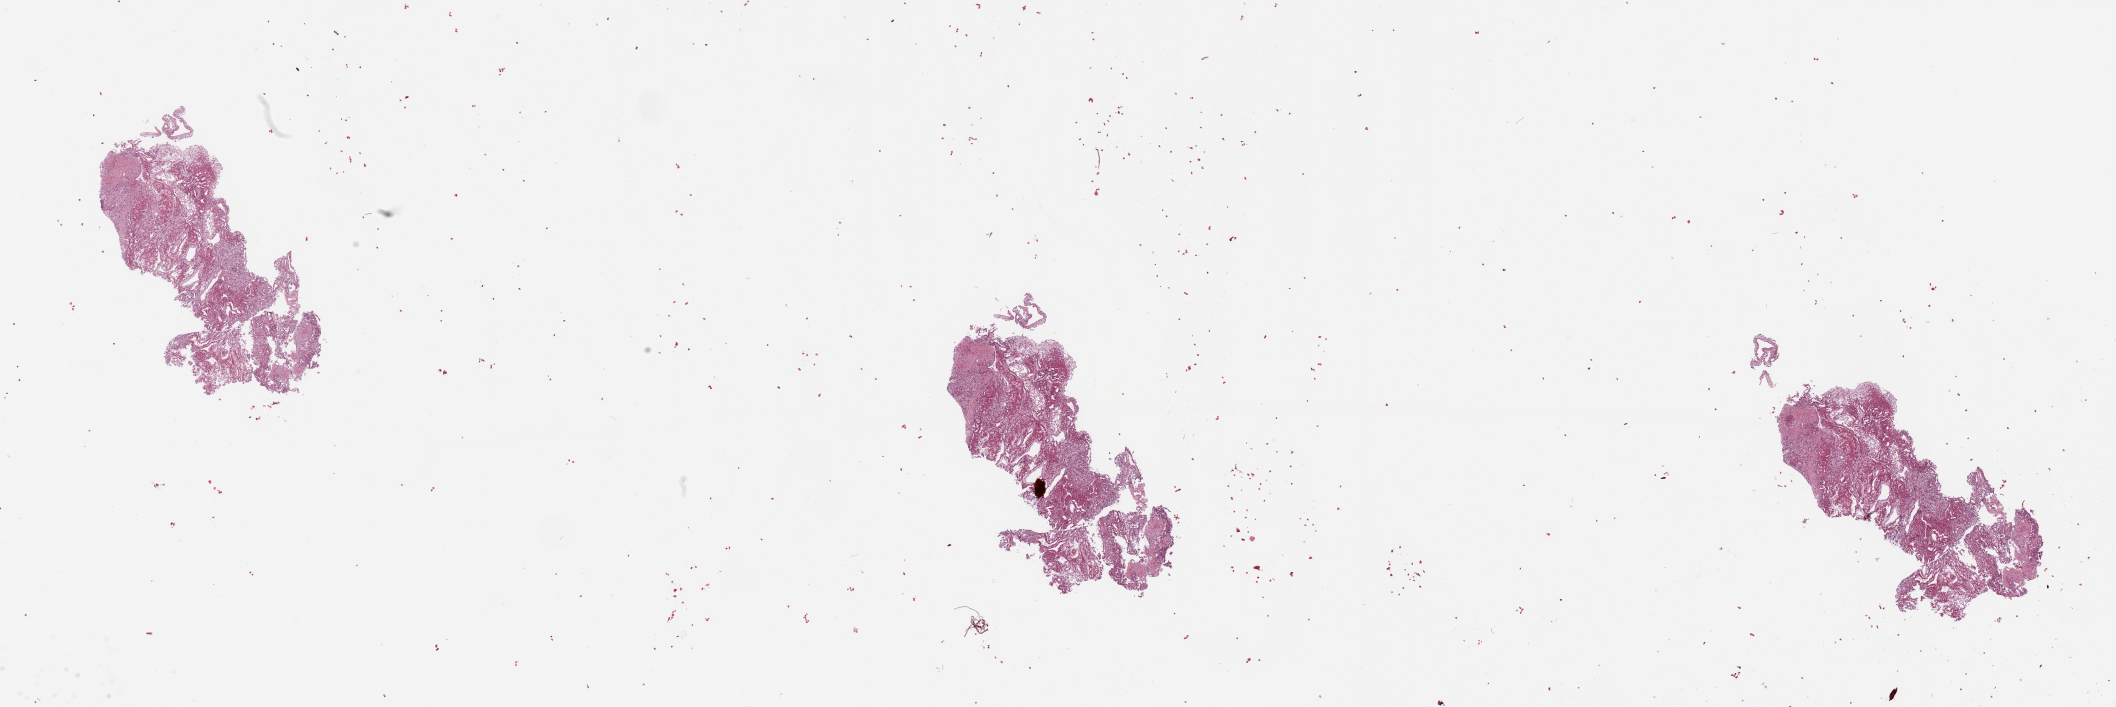
Digitized H&E-stained tissue section (whole slide), whole scanned area (about 33.5 x 11.2 mm, acquisition: 20x scan) shown as a low-resolution overview. Kidney, tumour tissue. 69-year-old male patient. Histologic grade: G3 (poorly differentiated).
• AJCC pathologic stage: III
• histologic diagnosis: Renal cell carcinoma, NOS
• primary tumour site (as recorded): upper pole